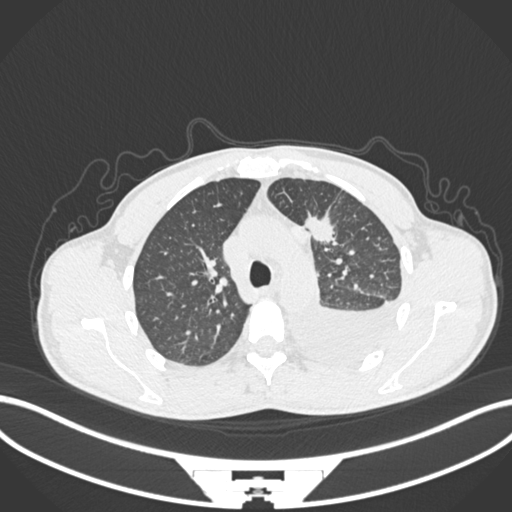
Chest CT, one axial slice. Reconstruction kernel B30f. Lung window (W 1500 / L -600 HU). 512 × 512 image matrix. Patient: male, 49 years. Case-level facts recorded for this patient, not image findings: clinical TNM (as recorded): T1c N1 M1.
Annotated regions visible in this slice (rectangle marked by the reading radiologist):
- lung tumour (recorded histology: adenocarcinoma): box from (x=306, y=211) to (x=337, y=248) px